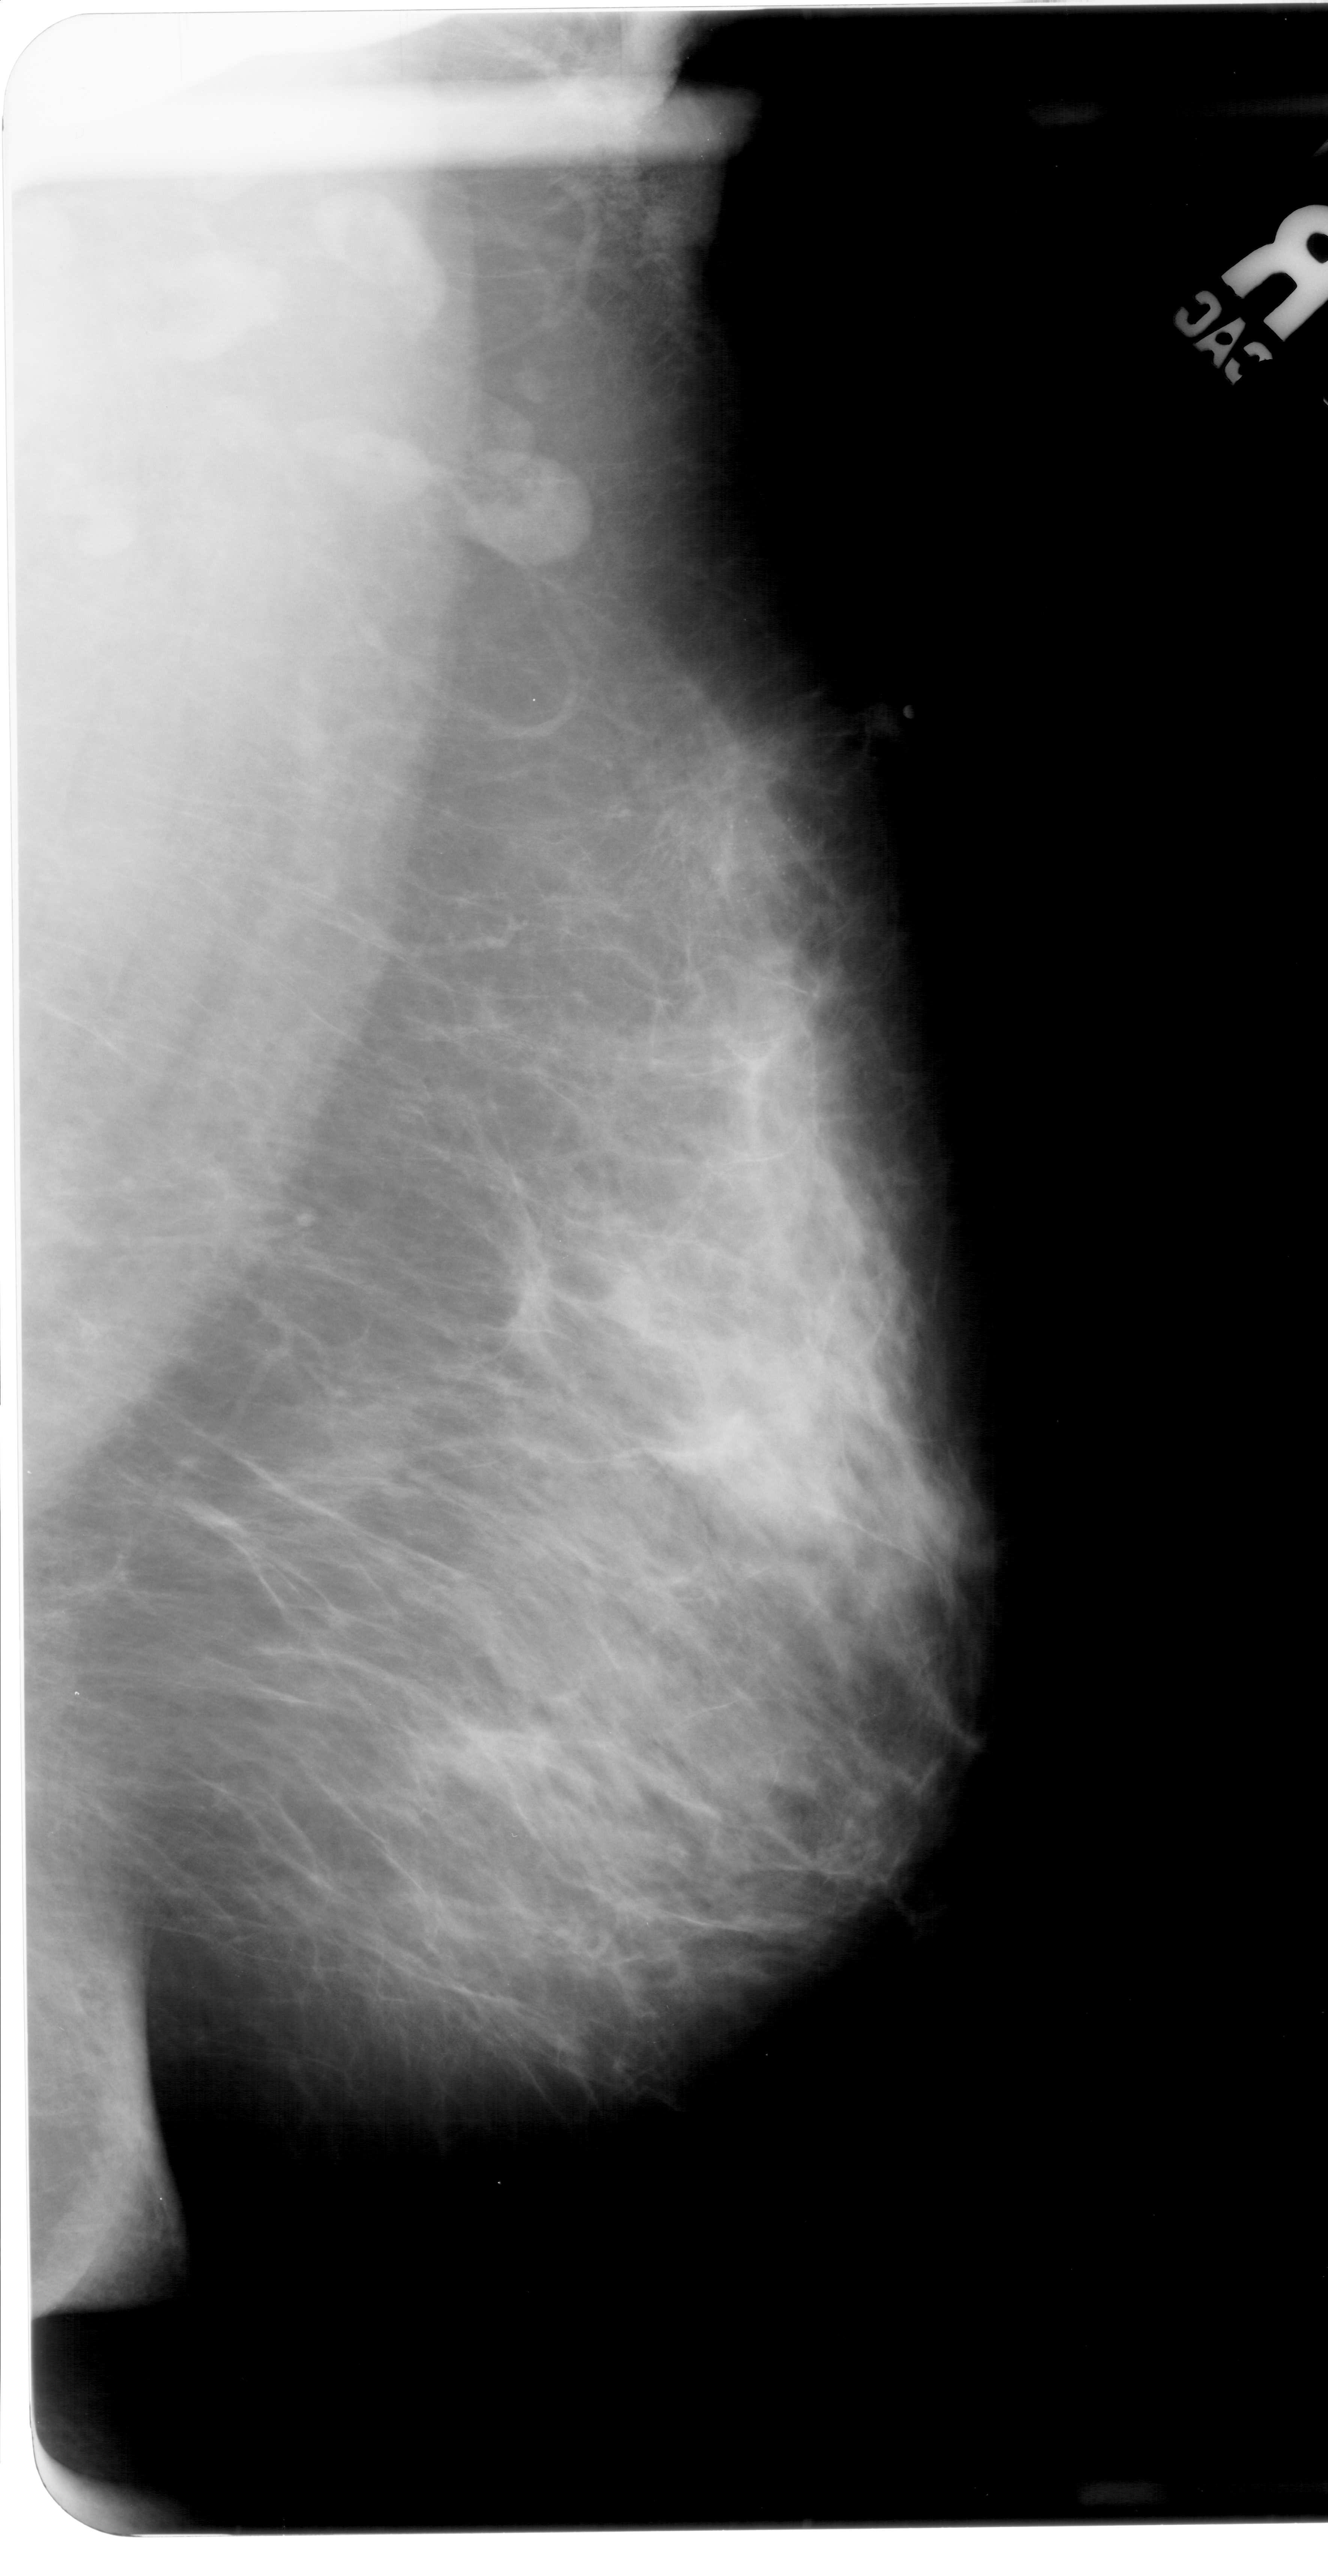
Mammogram (digitized film); right breast; MLO view; breast composition: heterogeneously dense (BI-RADS density category 3 of 4); 1328 × 2576 image matrix.
Marked abnormalities (boxes around the expert regions of interest):
- mass, shape irregular, margins spiculated; BI-RADS assessment category 5; subtlety rating 4 on a 1 (subtle) to 5 (obvious) scale; pathology (as recorded): malignant: bounding box <670,752,803,902> (left, top, right, bottom; pixels)